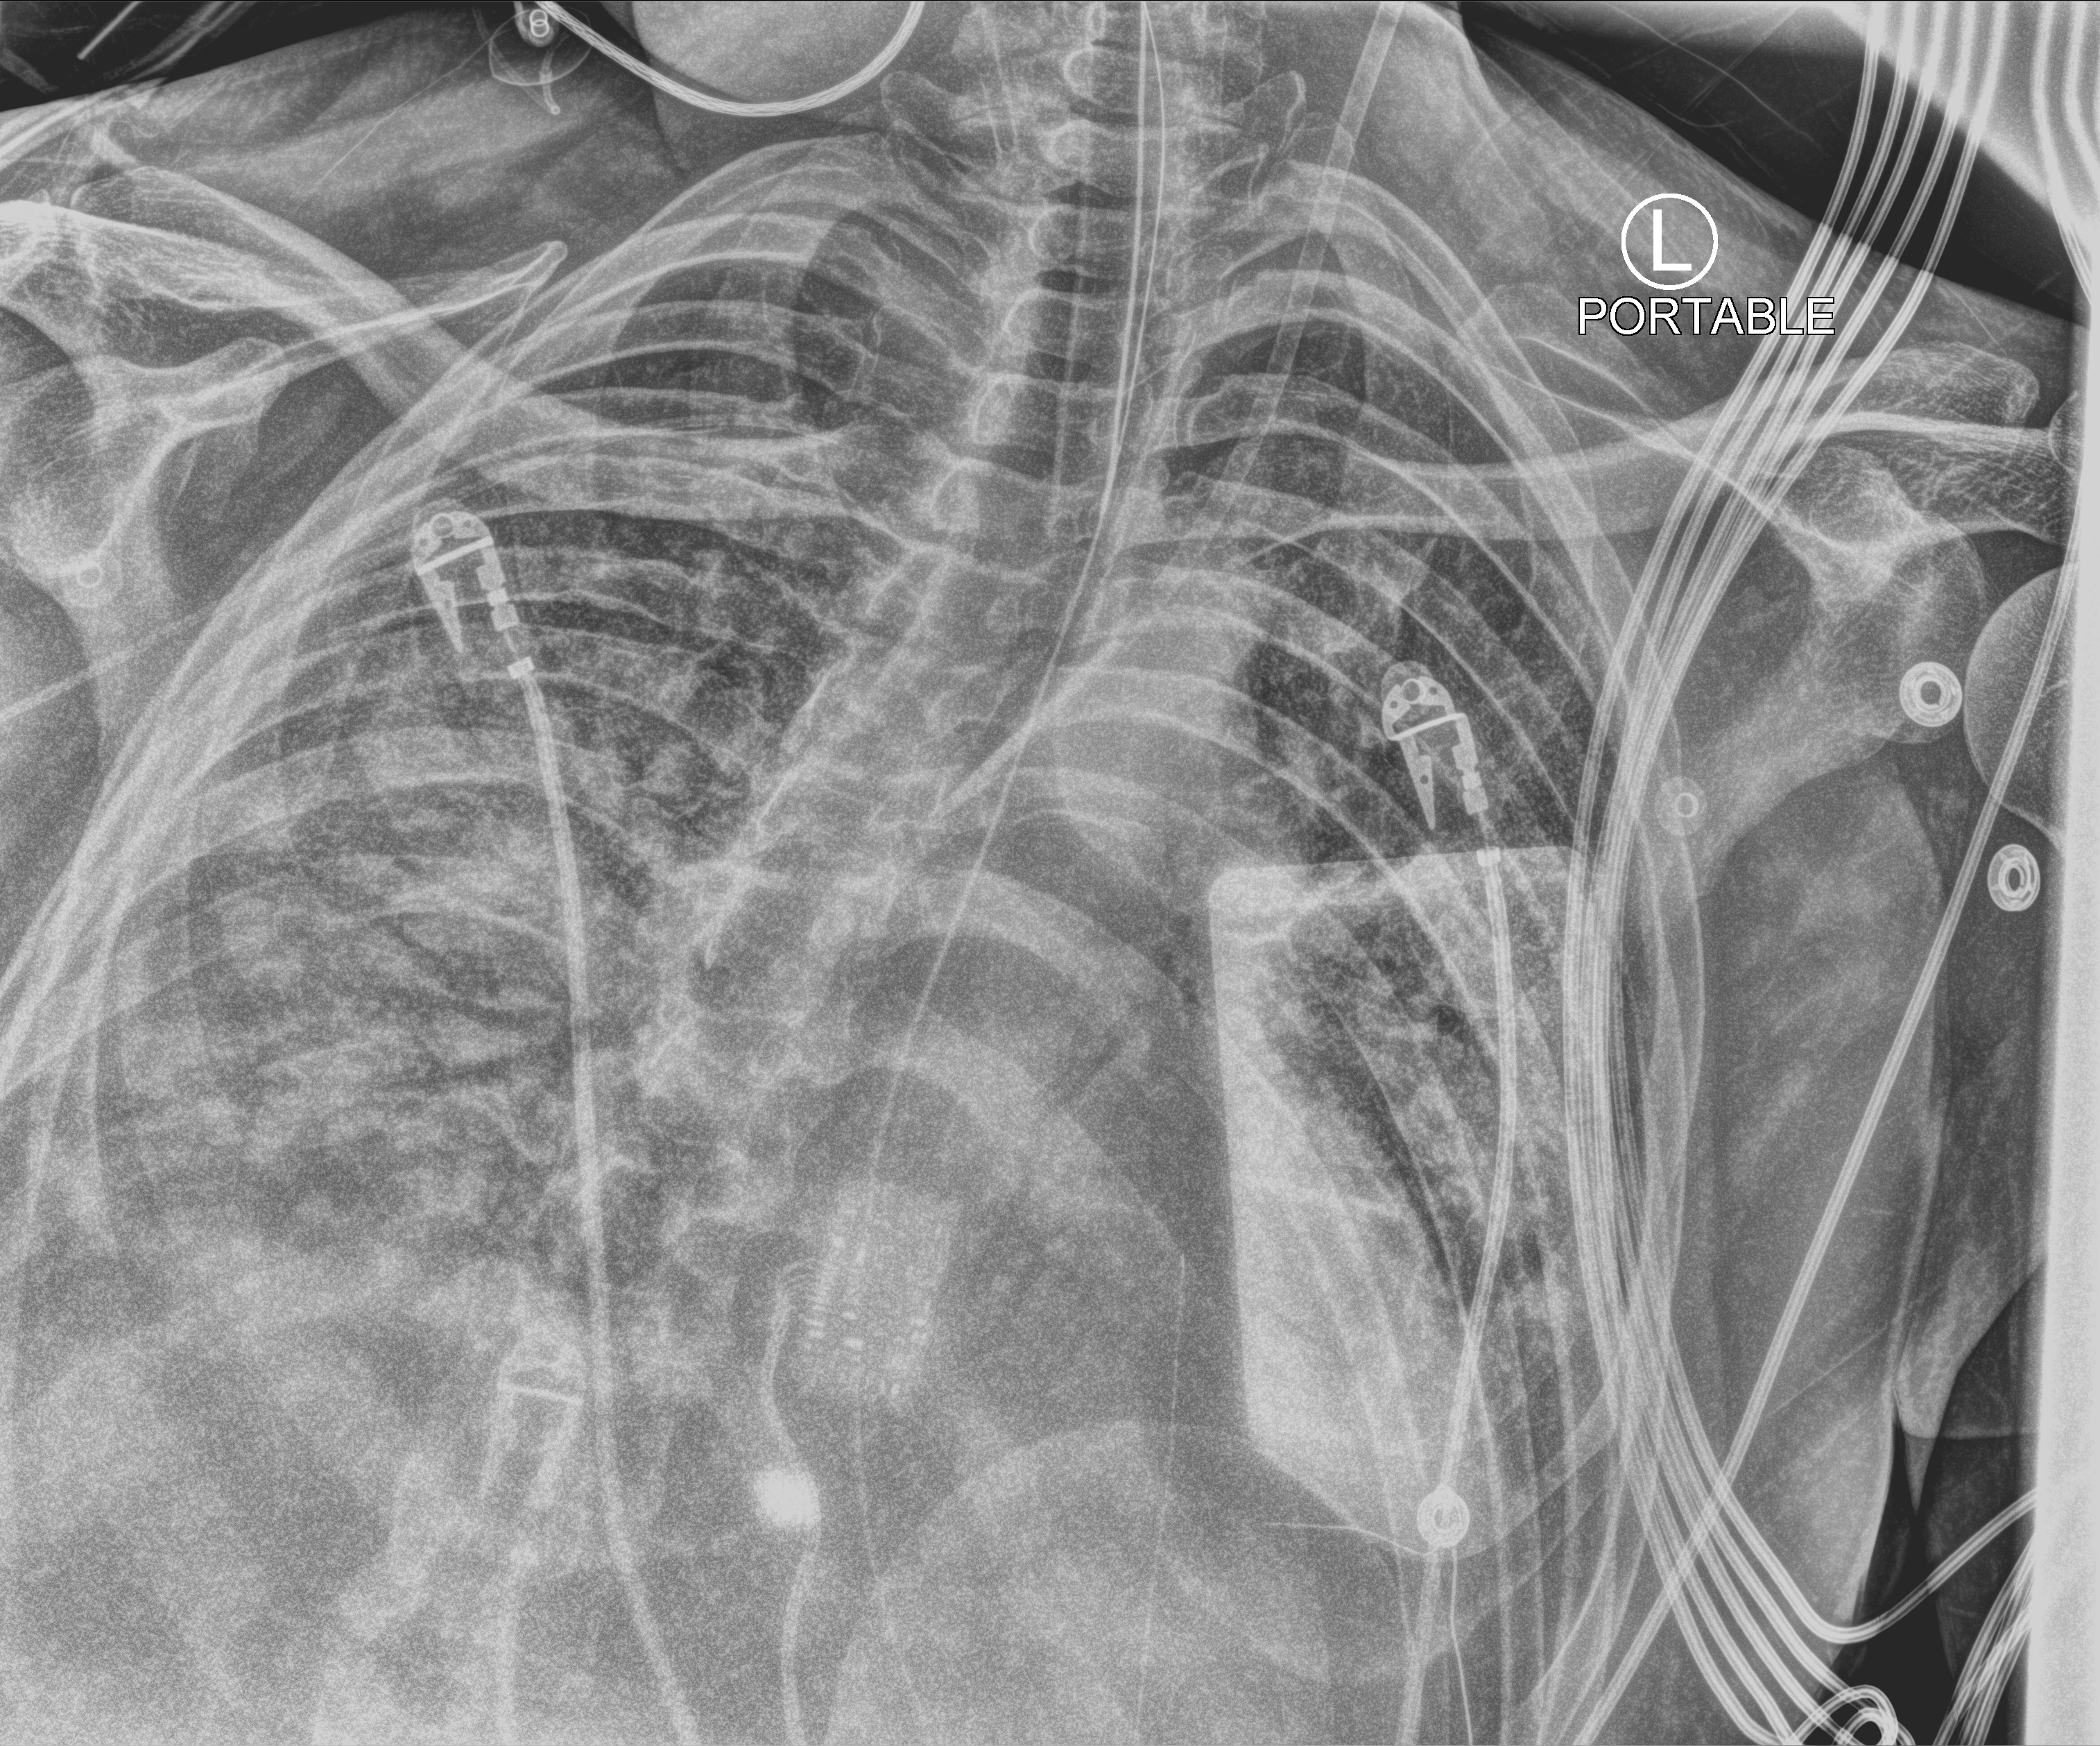
Chest X-ray (portable); anteroposterior (AP) projection. Patient hospitalised with COVID-19; male, aged 18–59 years.
Hospital-stay facts (about this admission, not read from this image; timing relative to this image not recorded):
- hypertension (admission record): no
- admitted to intensive care during this hospital stay: yes
- mechanically ventilated during this hospital stay: yes